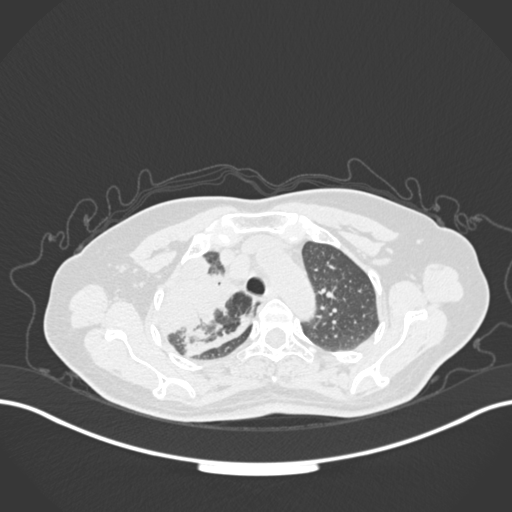
Chest CT, one axial slice. Position 125 of 177 along the scan axis. Reconstruction kernel B30f. 120 kVp. Lung window (W 1500 / L -600 HU). 1 mm slice thickness. 512 × 512 image matrix. Female patient, age 60 years. From the clinical record (not read from this slice): clinical TNM (as recorded): T3 N1 M1.
Outlined on this slice (rectangle marked by the reading radiologist):
- lung tumour (recorded histology: adenocarcinoma): bounding box <149,249,252,345> (left, top, right, bottom; pixels)